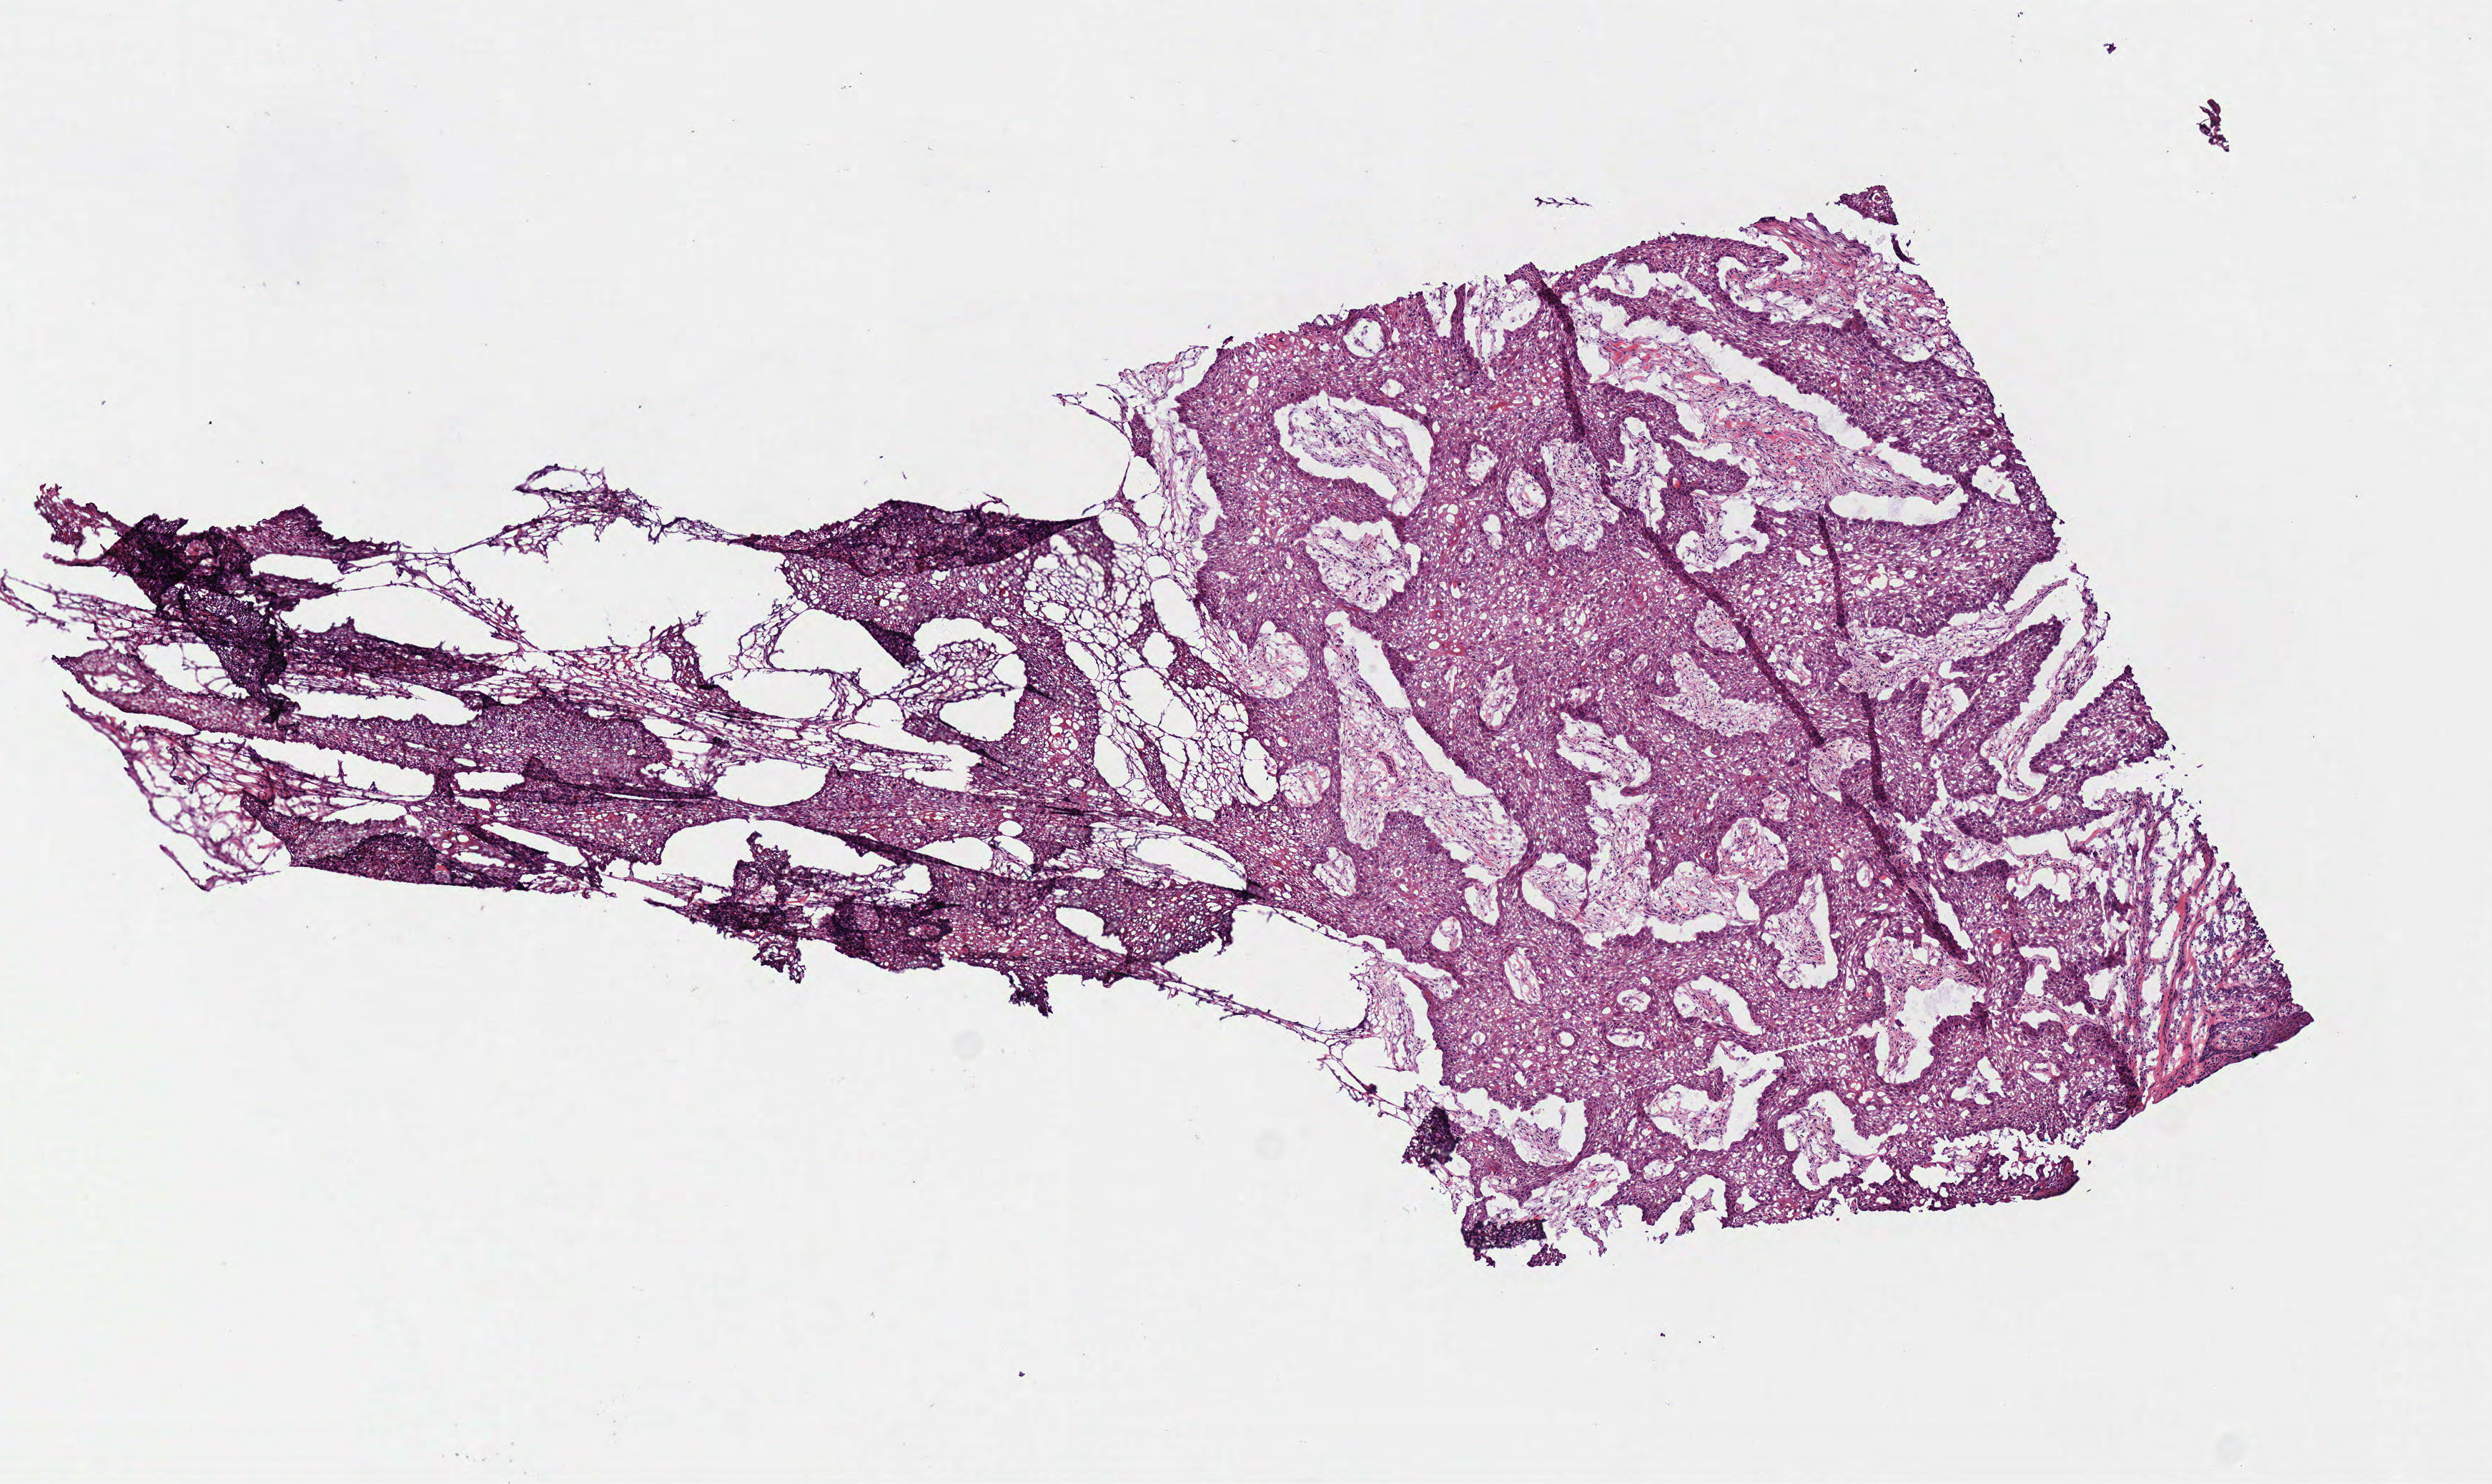
Digitized H&E-stained tissue section (whole slide), shown as a low-resolution overview of the whole scanned area (about 6.9 x 4.1 mm, acquisition: 40x scan), frozen section from the top of the tissue portion, primary tumour sample from the head and neck. Male, age 54 years at initial diagnosis. Histologic grade: G3 (poorly differentiated). Pathologist review of this section (percent, as recorded): tumour cells 85%, tumour nuclei 80%, normal cells 0%, stromal cells 15%, necrosis 0%.
* diagnosis: Squamous cell carcinoma, NOS (overlapping lesion of lip, oral cavity and pharynx)
* AJCC pathologic stage: I (7th edition)